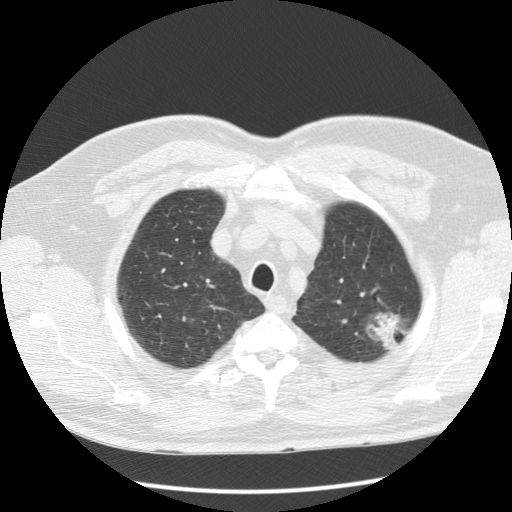
Low-dose screening chest CT, one axial slice; position 103 of 123 along the scan axis; reconstruction kernel STANDARD; lung window (W 1500 / L -600 HU); 512 × 512 image matrix.
Structures marked on this image (expert manual segmentation):
- lesion 1 (tumor, upper lobe of left lung): bounding box [x1, y1, x2, y2] px = [374, 315, 396, 348]